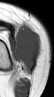
MRI of an extremity soft-tissue mass, one axial slice. Slice 20 of 42 in the series (ordered by position). MR volume resampled by the dataset authors to the PET/CT grid (not the native acquisition matrix). 3.27 mm slice thickness. 54 × 97 image matrix, field of view 53 × 95 mm. Female patient. From the clinical record (not read from this slice): histological type: spindle cell suggestive of biphasic synovial sarcoma; grade: intermediate; site of the primary tumour: left knee.
Outlined on this slice (expert contour drawn on MRI and transferred to this co-registered scan by the dataset authors):
- gross tumour volume including surrounding oedema: bounding box <14,25,41,74> (left, top, right, bottom; pixels)
- gross tumour volume (mass): <14,28,41,74>